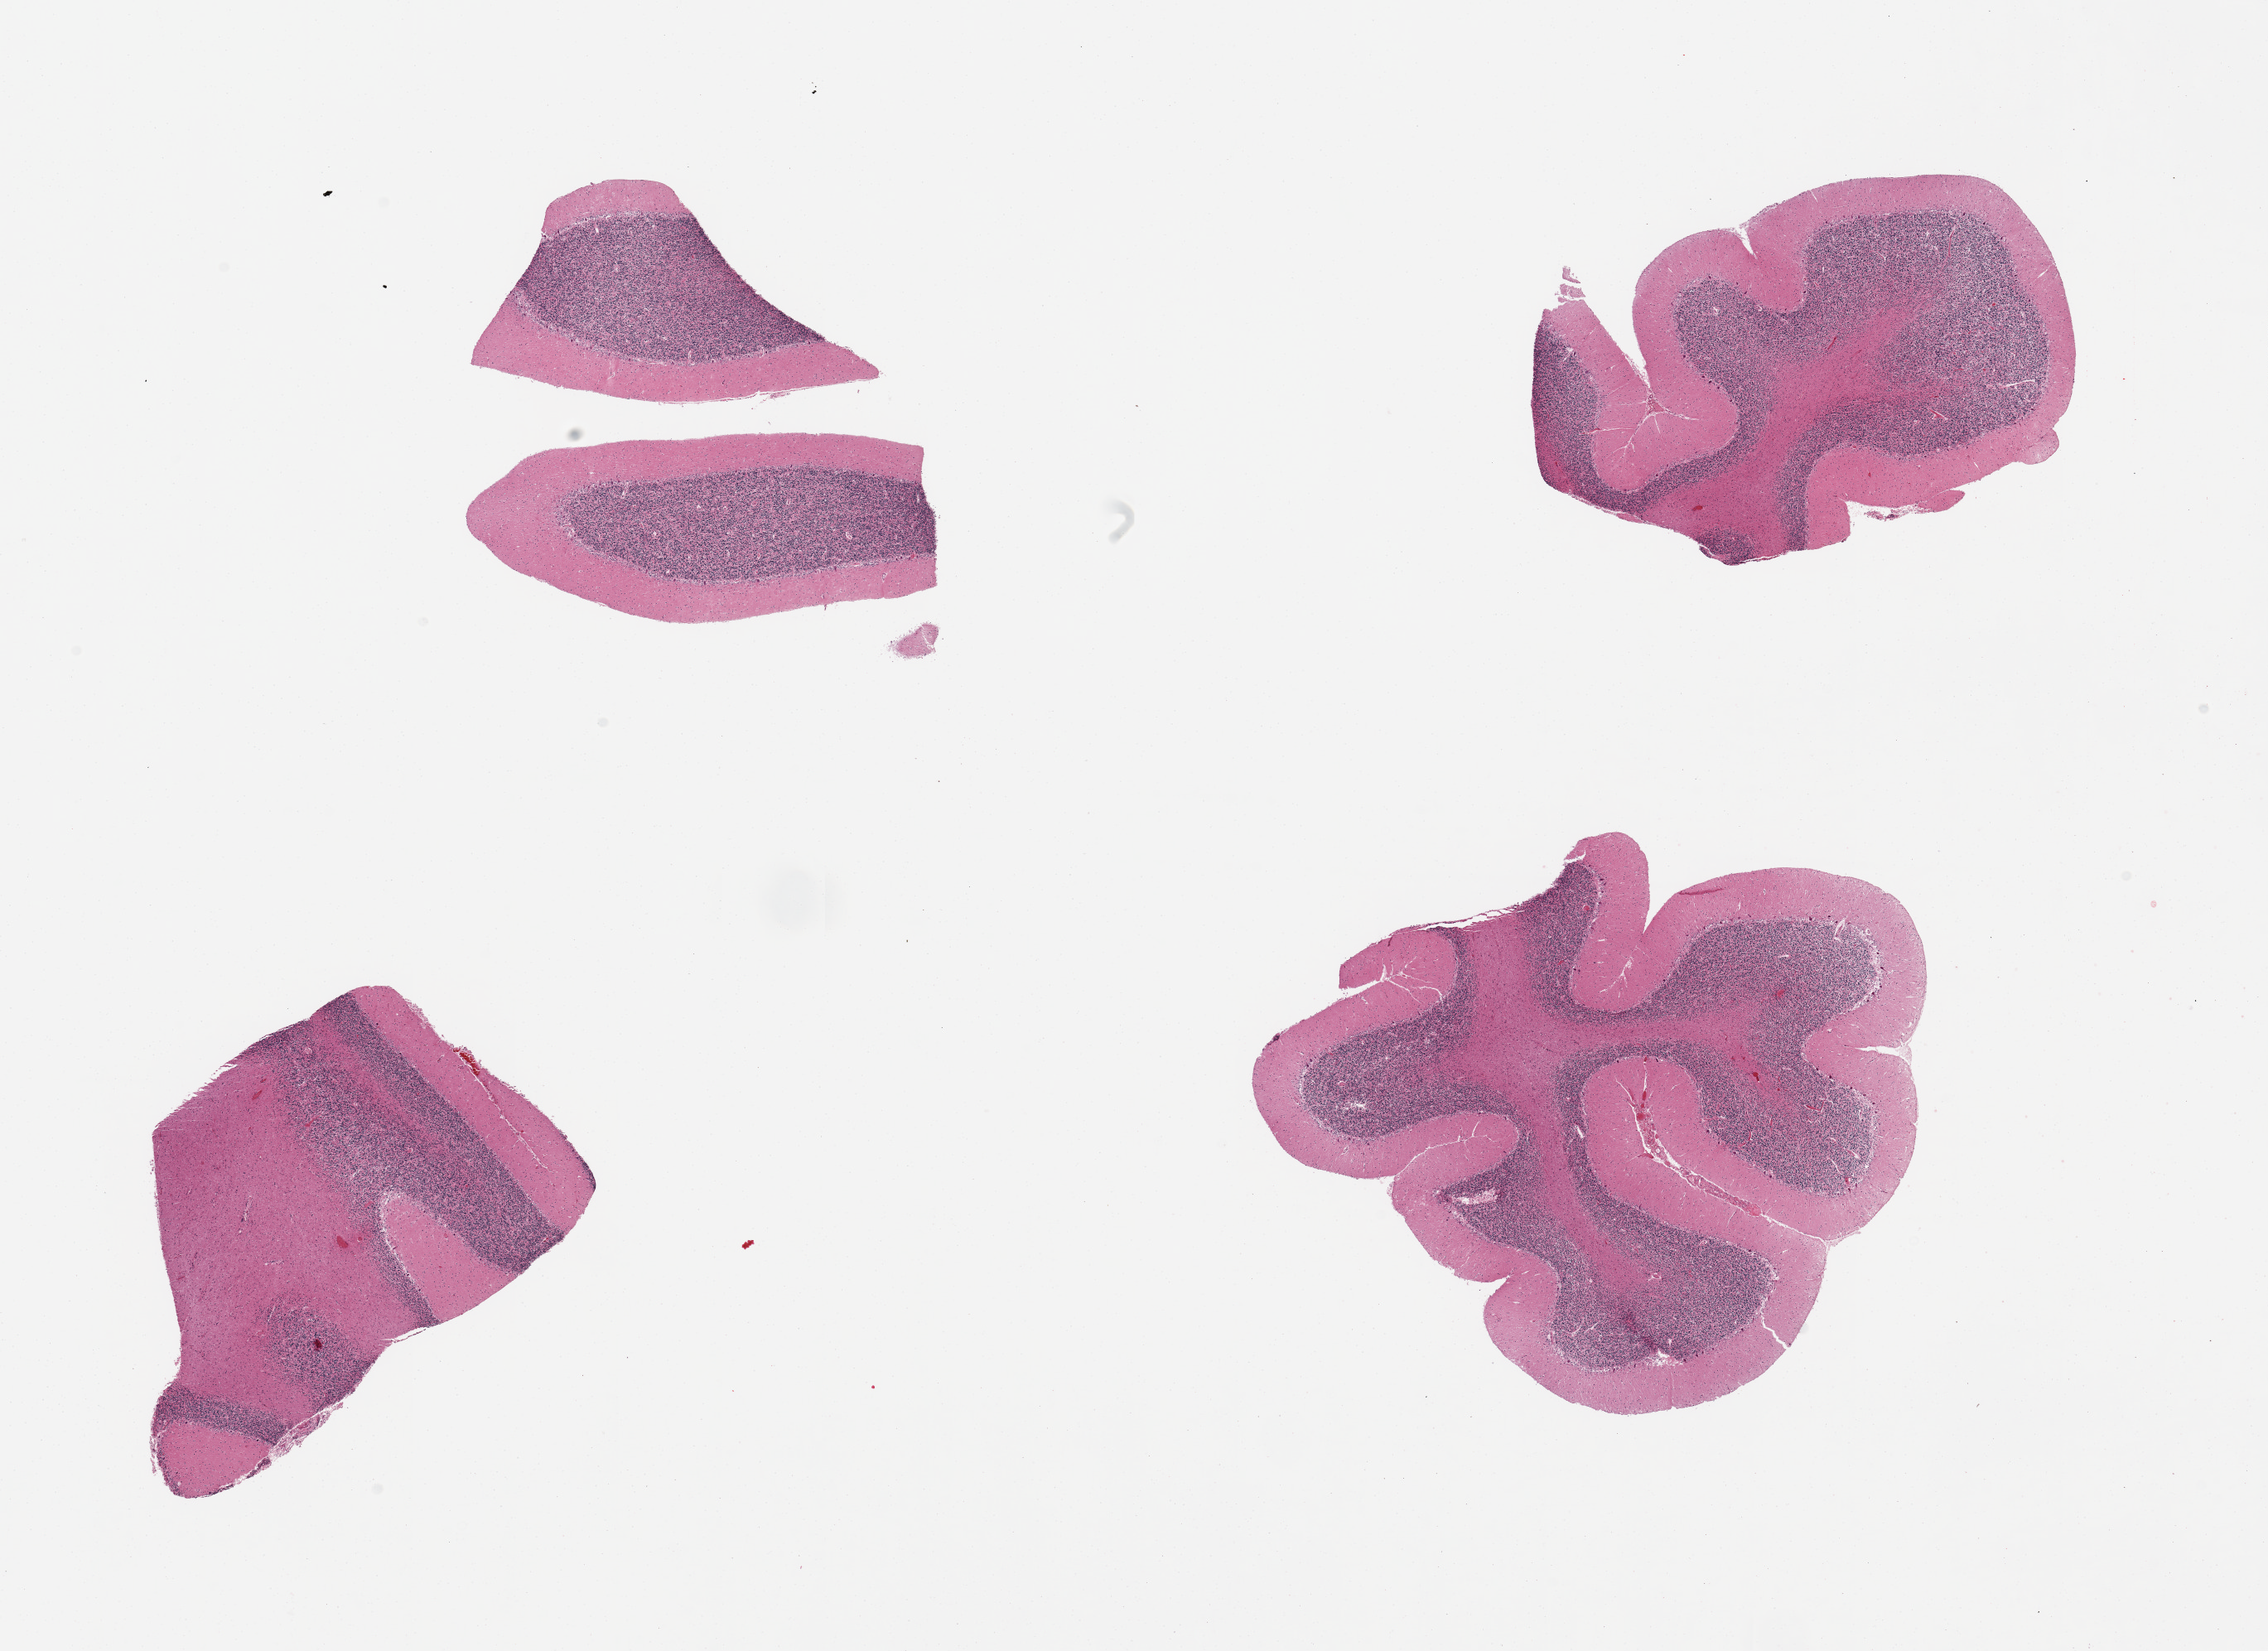
Whole-slide image, H&E stain — whole scanned area (about 21.7 x 15.8 mm) shown as a low-resolution overview. PAXgene-fixed, paraffin-embedded tissue. Target tissue: cerebellum. Tissue donor sample. Donor: male.
- reviewer comment on this tissue sample: 4 pieces